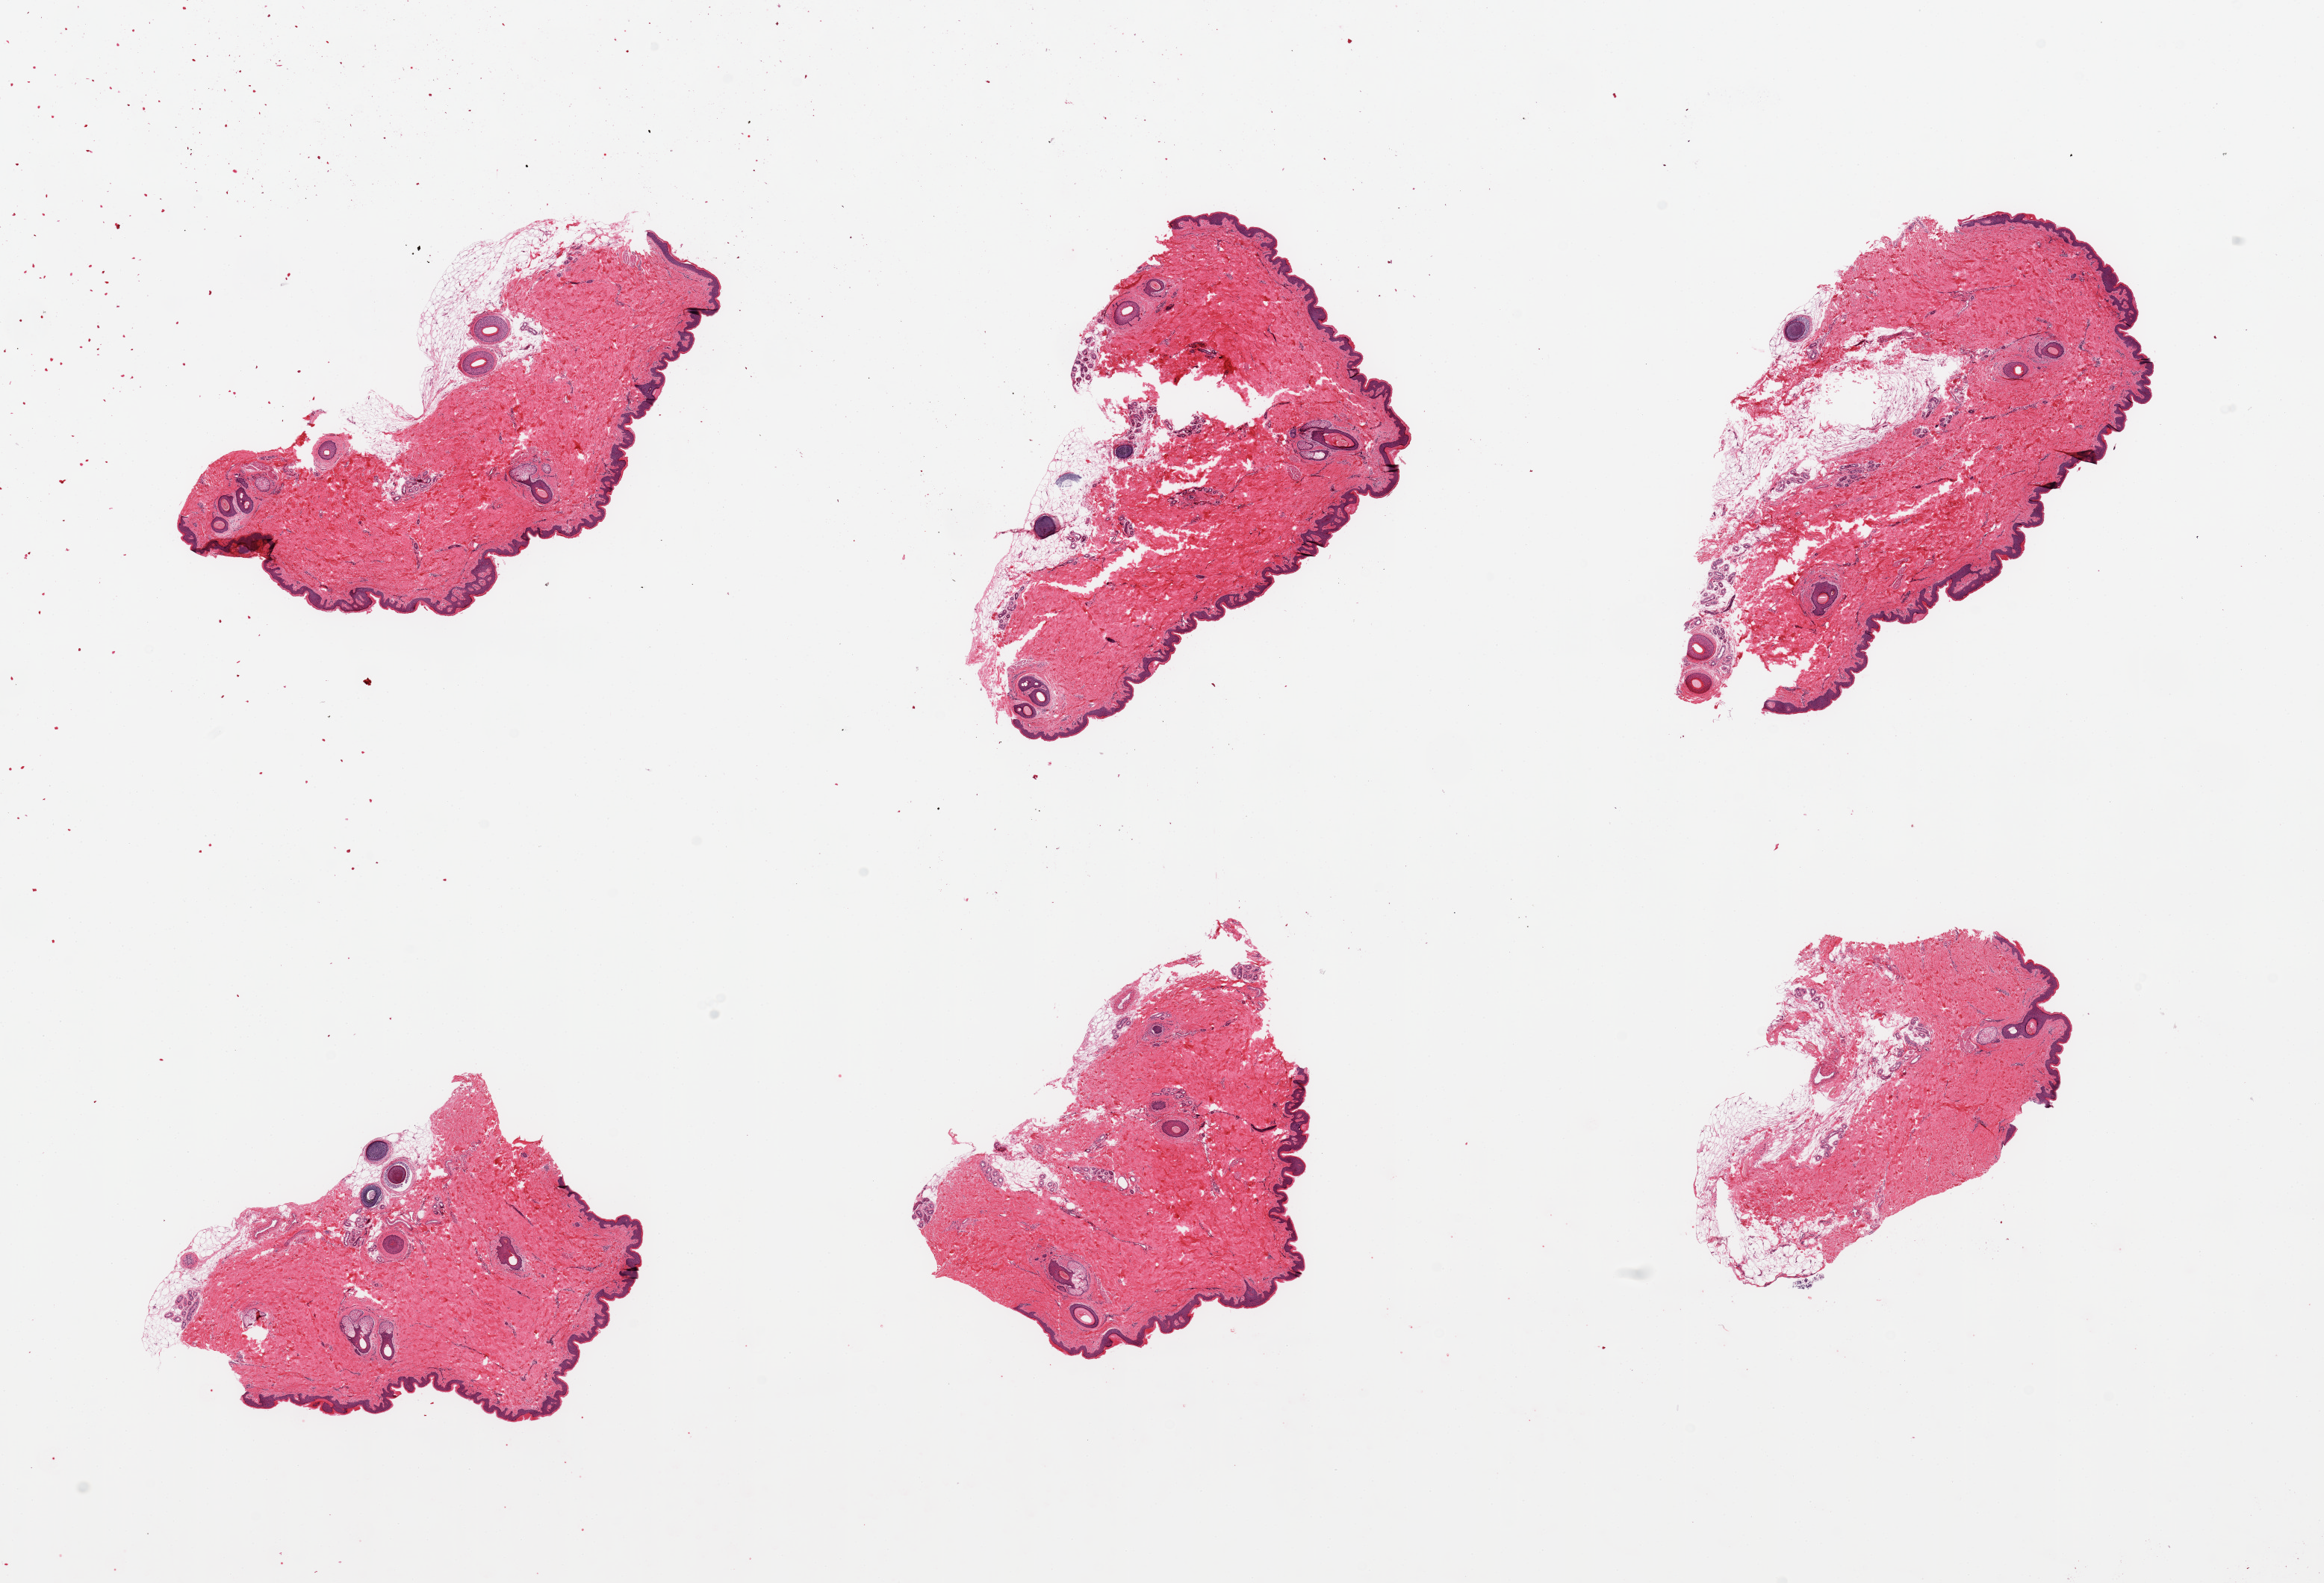
Whole-slide image, H&E stain — shown as a low-resolution overview of the whole scanned area (about 24.6 x 16.8 mm), PAXgene-fixed, paraffin-embedded tissue, sampled site (target tissue): skin of suprapubic region, donor tissue sample.
* pathologist's review note for this sample: 6 pieces; hair-bearing skin sampled; up to 20% dermal fat